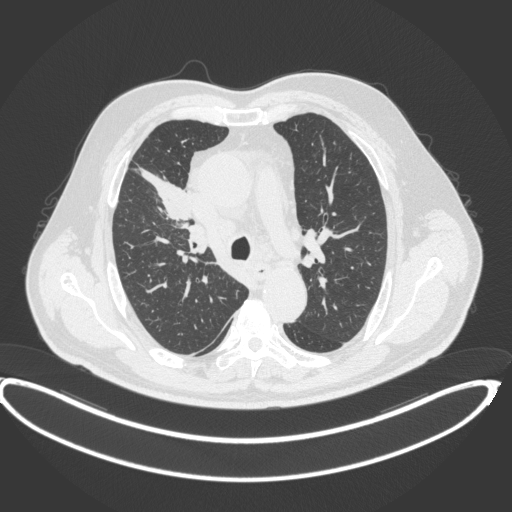
Chest CT, one axial slice. Slice 279 of 395 in the series (ordered by position). Reconstruction kernel B31f. Lung window (W 1500 / L -600 HU). 1 mm slice thickness. 512 × 512 image matrix, field of view 448 × 448 mm. Patient: male, 62 years. Case-level facts recorded for this patient, not image findings: clinical TNM (as recorded): T1c N3 M1c.
Structures marked on this image (bounding box drawn by a radiologist):
- lung tumour (recorded histology: adenocarcinoma): bounding box [x1, y1, x2, y2] px = [139, 165, 192, 225]